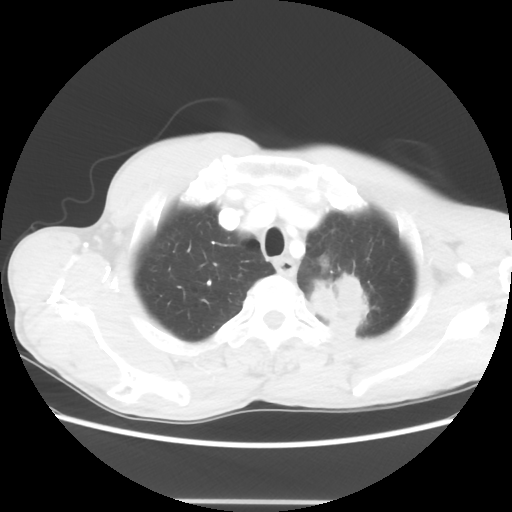
Chest CT, one axial slice; position 56 of 62 along the scan axis; reconstruction kernel STANDARD; lung window (W 1500 / L -600 HU); 5 mm slice thickness; 512 × 512 image matrix, field of view 360 × 360 mm. Patient: male, 61 years. Case-level facts recorded for this patient, not image findings: clinical TNM (as recorded): T3 N1 M1.
Annotated regions visible in this slice (bounding box drawn by a radiologist):
- lung tumour (recorded histology: adenocarcinoma): bounding box [x1, y1, x2, y2] px = [302, 265, 372, 345]